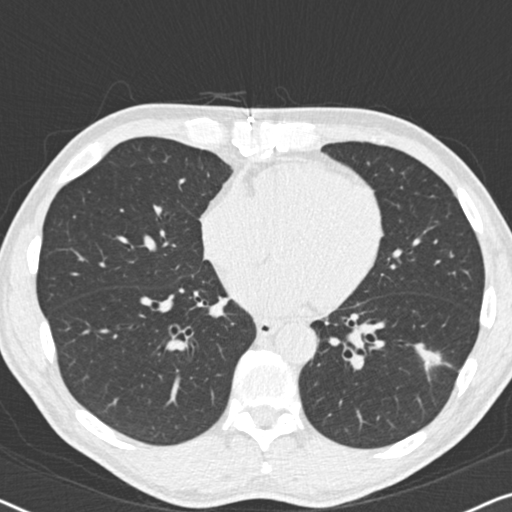
Chest CT (low-dose screening protocol), one axial image; second screening round (one year after baseline); lung window (W 1500 / L -600 HU); 2 mm slice thickness; 120 kVp; slice 117 of 208 in the series; 512 × 512 image matrix. Male, age 59 years at enrolment.
- Expert reader's lesion annotation, bounding box [x1, y1, x2, y2] px = [410, 334, 465, 383].
- The screening reader recorded 2 non-calcified nodules or masses ≥4 mm on this exam (left lower lobe, right middle lobe); which of them this box marks is not recorded.
- Official screen result: positive, other.
- Later outcome: lung cancer diagnosed 484 days after this screen — adenocarcinoma, NOS, left lower lobe, poorly differentiated (G3), stage IA (AJCC 6th edition), 20 mm at pathology.